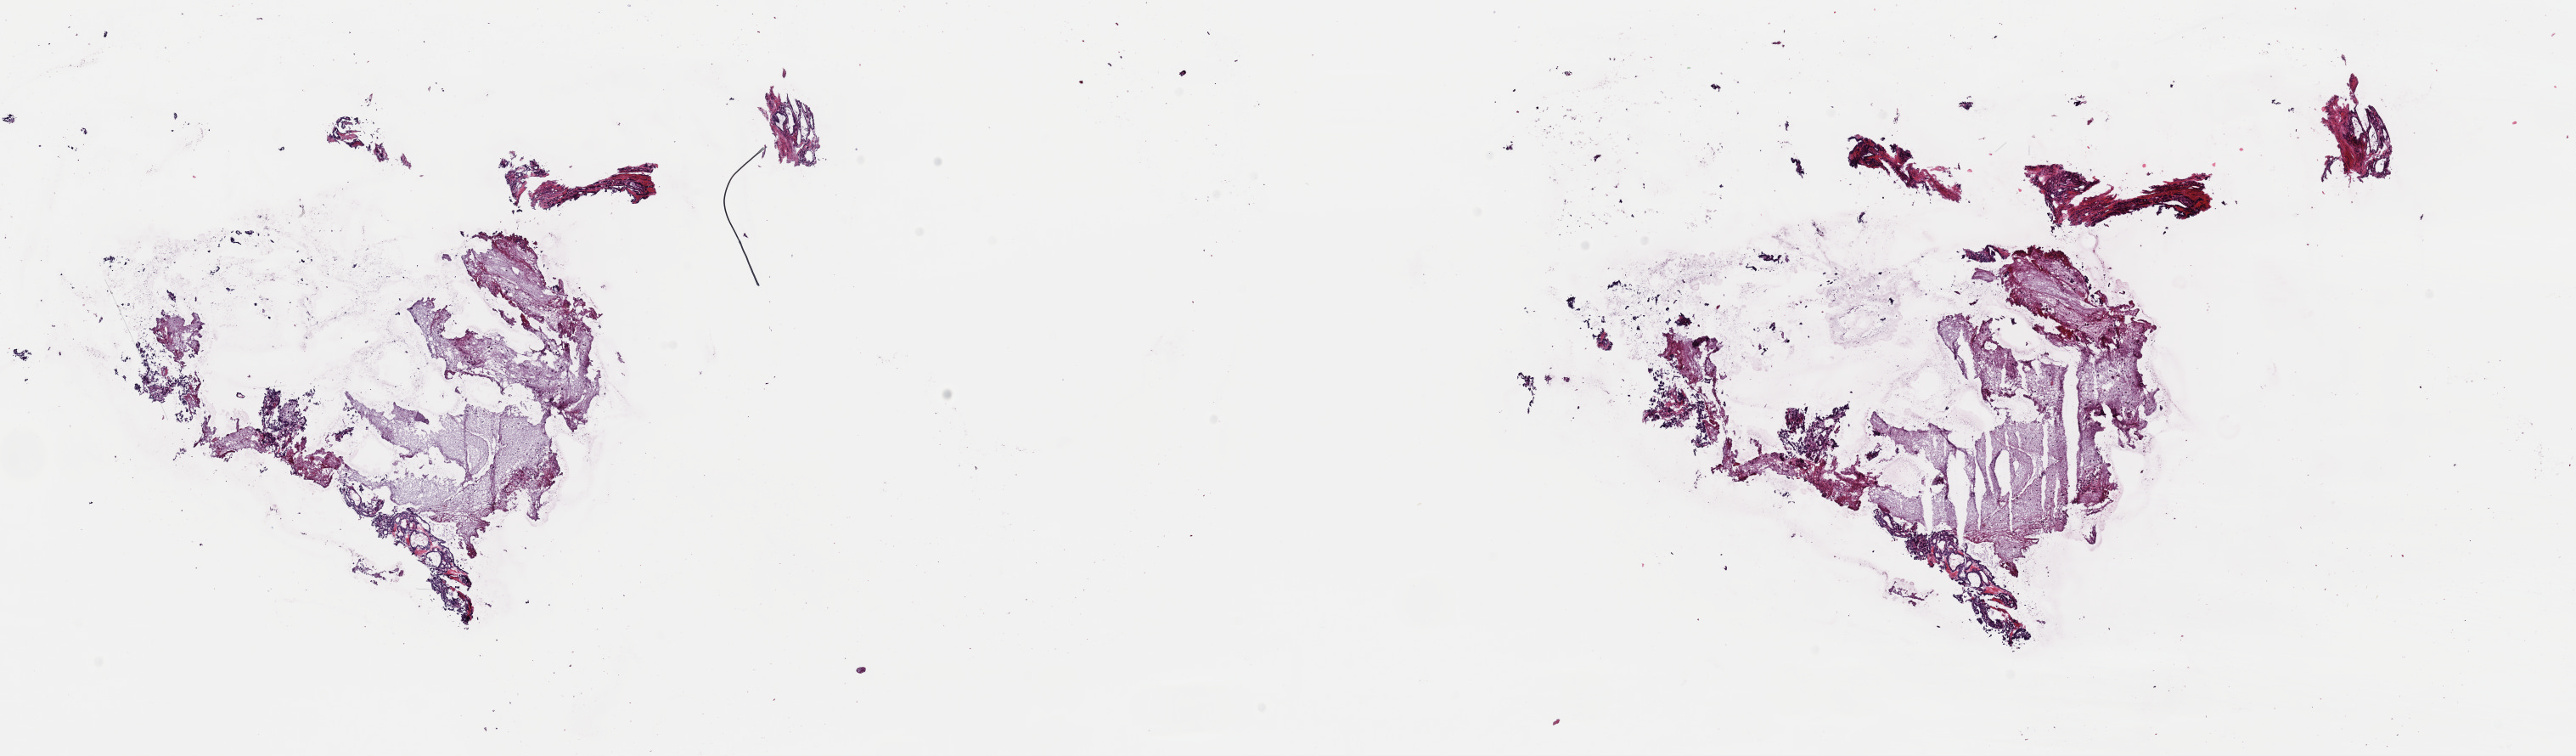
H&E whole-slide image — shown as a low-resolution overview of the whole scanned area (about 24.0 x 7.0 mm), frozen section, sample: primary tumour, thyroid. Female, age 43 years at initial diagnosis. Pathologist review of this section (percent, as recorded): tumour cells 10%, tumour nuclei 80%, normal cells 0%, stromal cells 90%, necrosis 0%. Infiltration values recorded for this section: lymphocyte infiltration 0%, monocyte infiltration 0%, neutrophil infiltration 0%.
TNM: T2 NX MX. AJCC pathologic stage: I (6th edition). Laterality: left. Pathologic diagnosis: Papillary adenocarcinoma, NOS (thyroid gland).